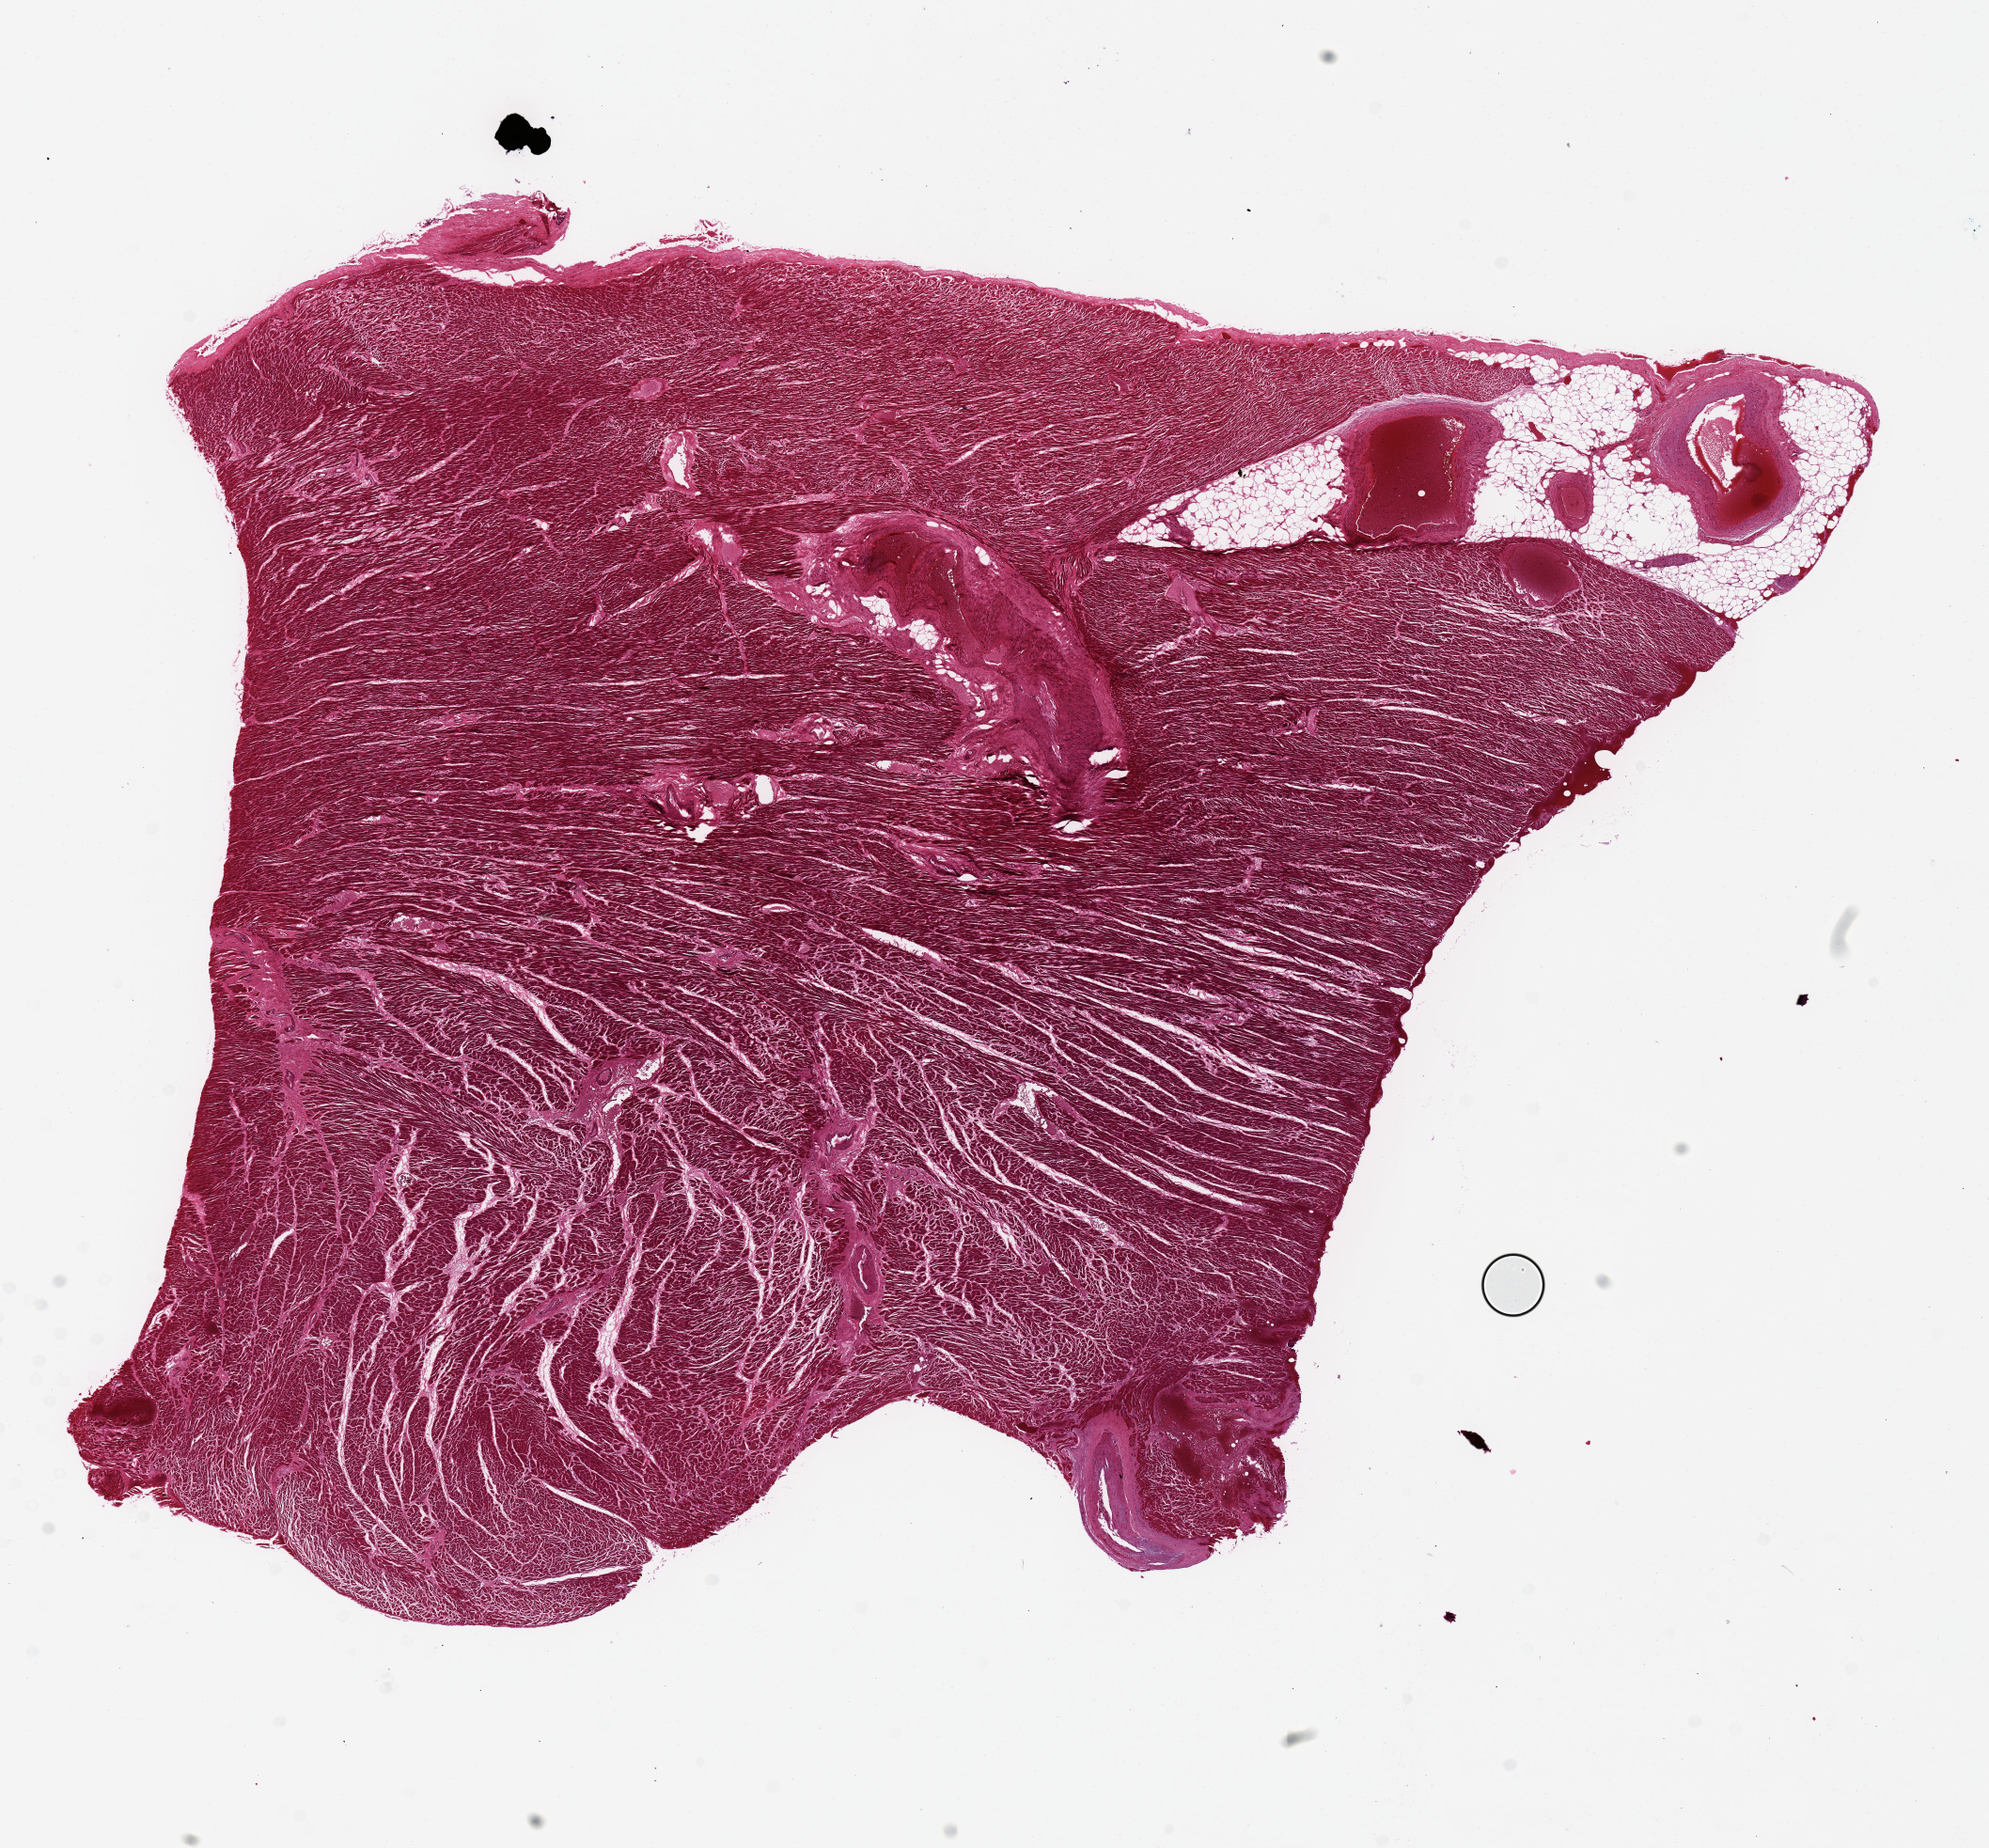
Whole-slide image, H&E stain — low-resolution overview of the scanned area, about 16.7 x 15.5 mm (from a 20x scan); PAXgene-fixed, paraffin-embedded tissue; section of heart (target tissue); donor tissue sample. Donor: male.
* pathologist's review note for this sample: 7% fat